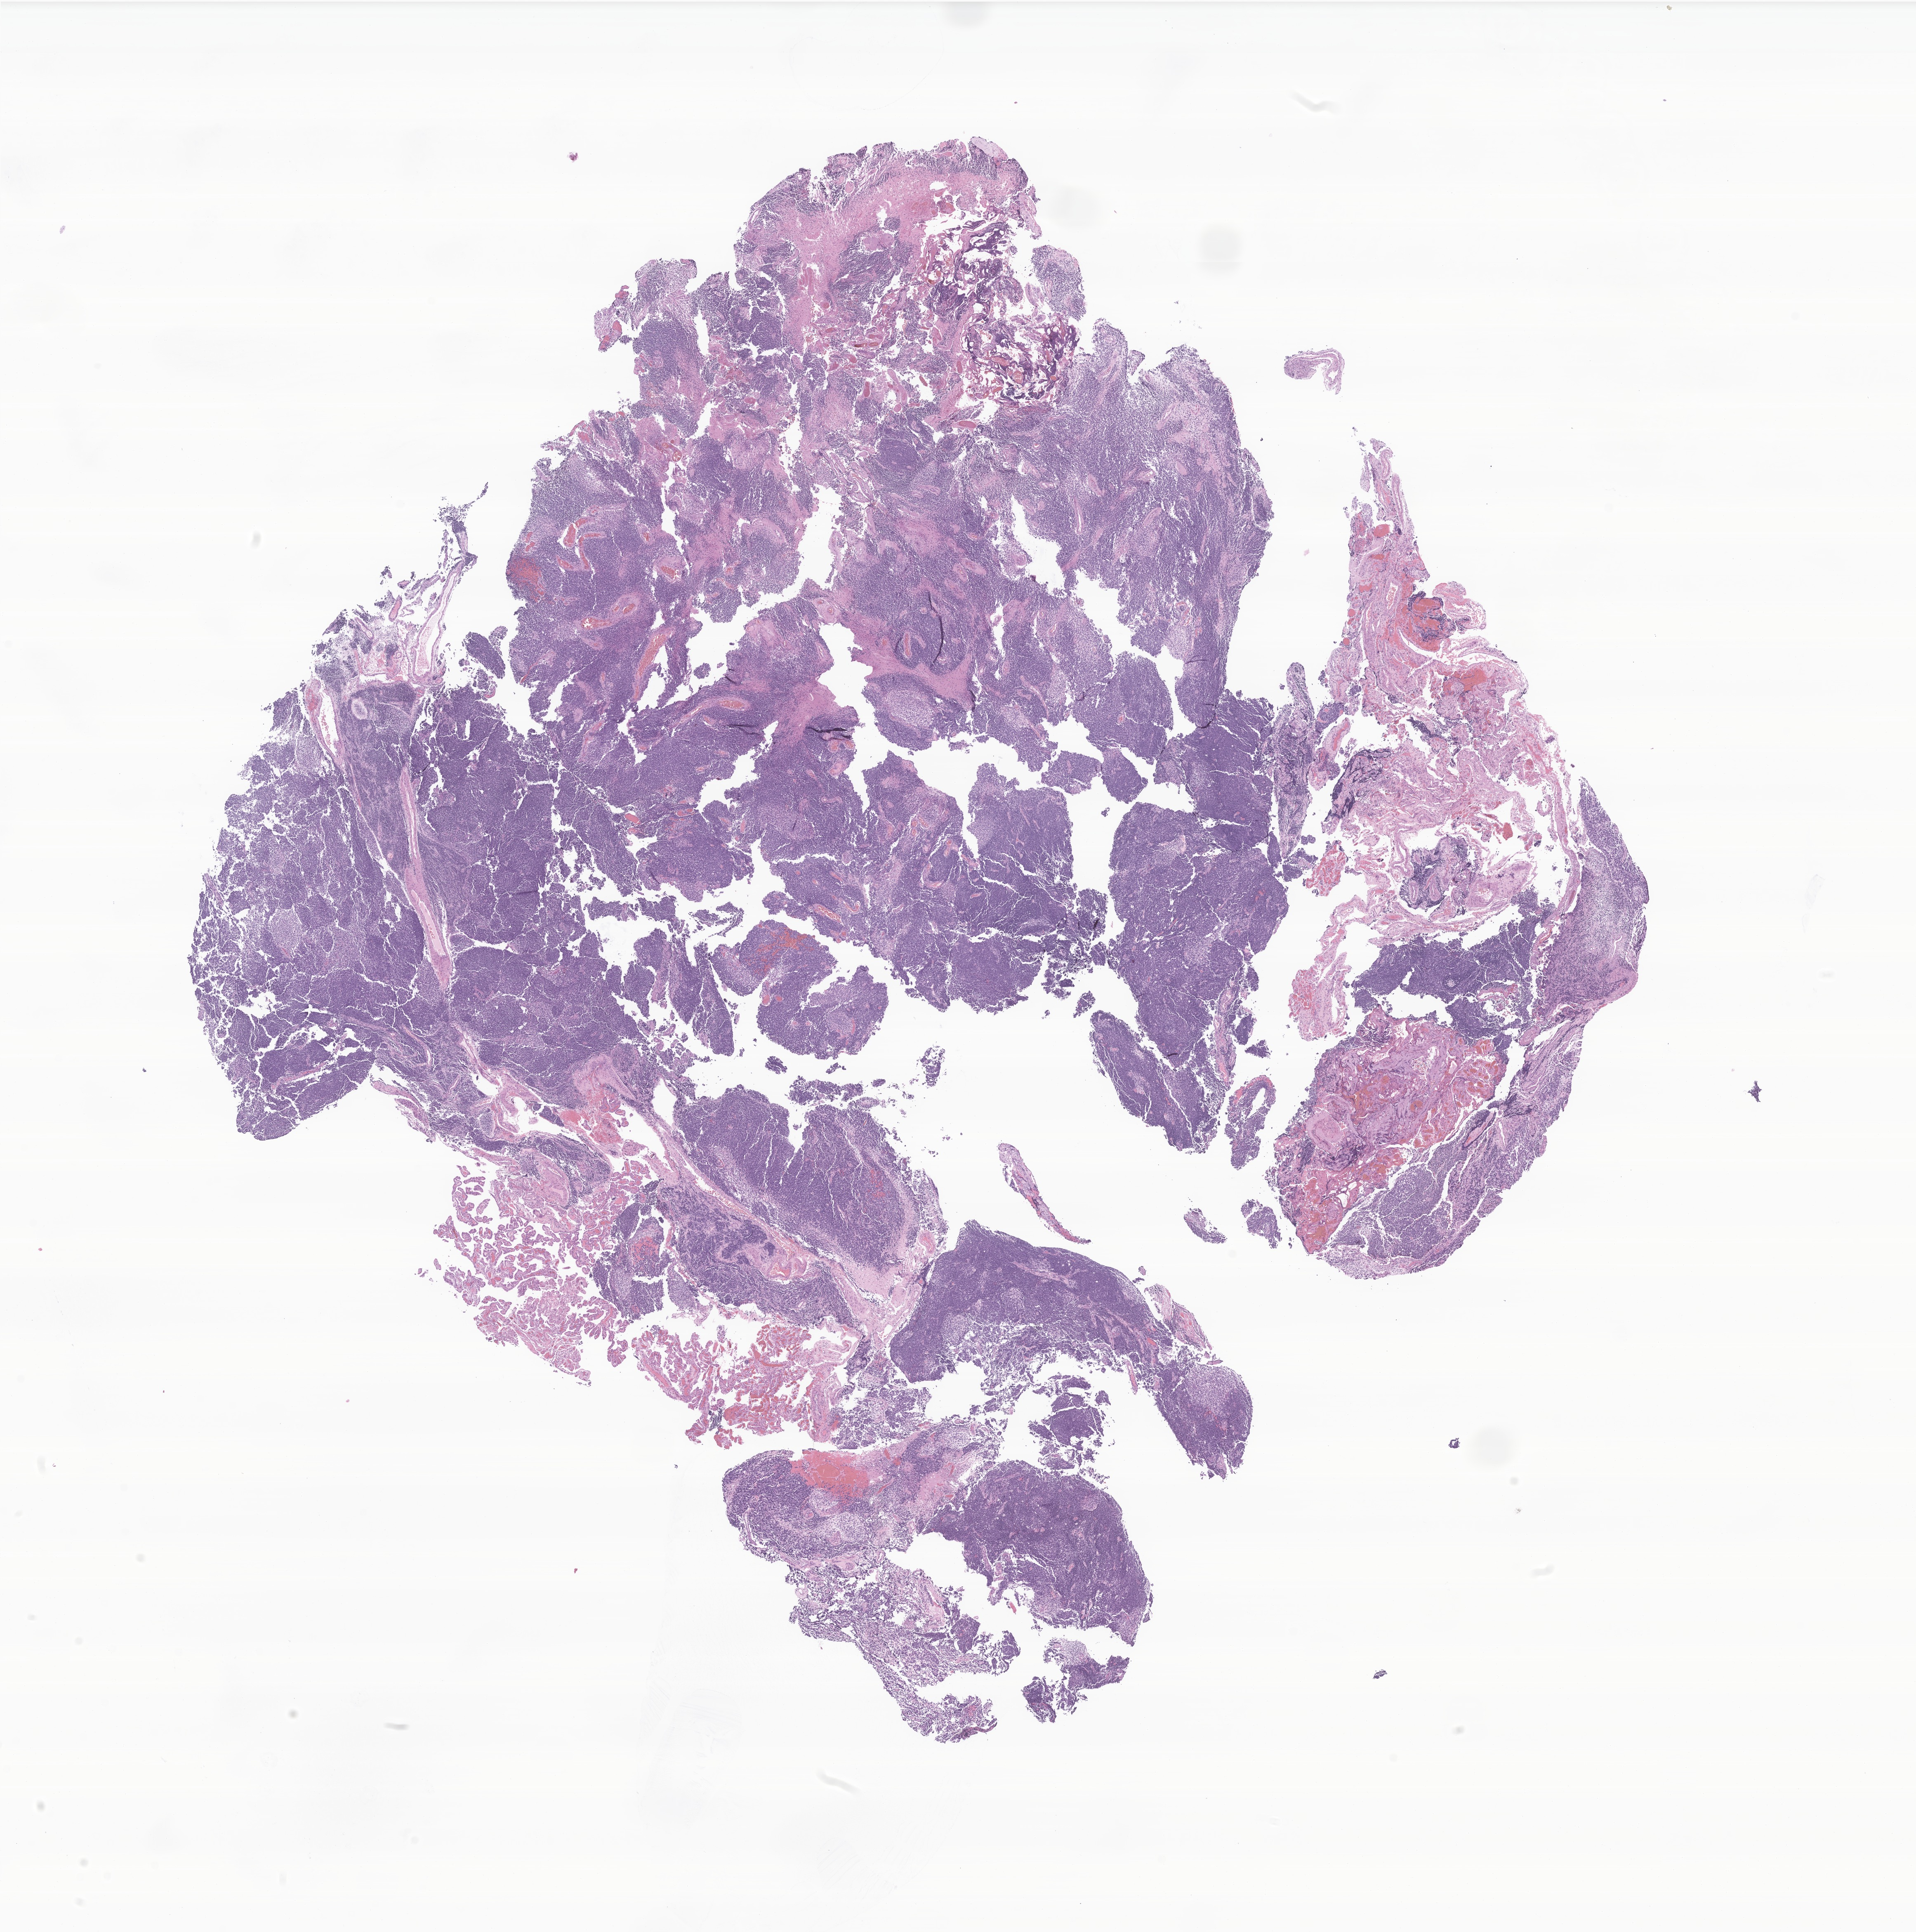
Haematoxylin and eosin whole-slide image of tumor tissue from the brain — low-resolution overview of the scanned area, about 19.6 x 19.7 mm. Formalin-fixed, paraffin-embedded (FFPE) tissue. Female patient, age 59 months.
Diagnosis: Medulloblastoma, NOS.